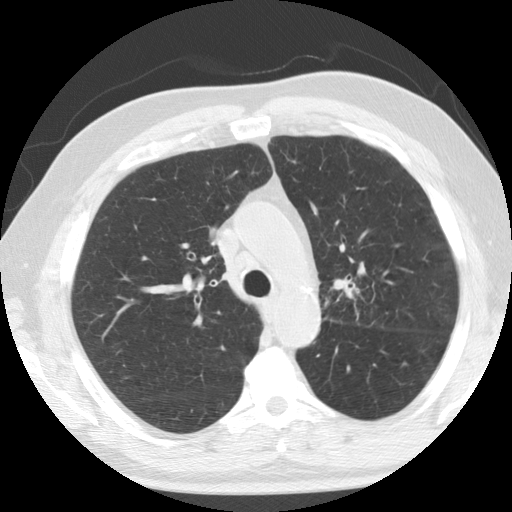
Low-dose screening chest CT, axial slice; second screening round (one year after baseline); lung window (W 1500 / L -600 HU); 2.5 mm slice thickness; slice 42 of 133 in the series; 512 × 512 image matrix, field of view 342 × 342 mm. Male participant, aged 74 years at enrolment.
Expert-annotated lung lesion, box from (x=305, y=262) to (x=371, y=325) px. Screening reader's record for this exam: no non-calcified nodule ≥4 mm recorded. Official screen result: positive, other. Participant outcome: lung cancer diagnosed 274 days after this screen — non-small cell carcinoma, left upper lobe, poorly differentiated (G3), stage IIB (AJCC 6th edition).